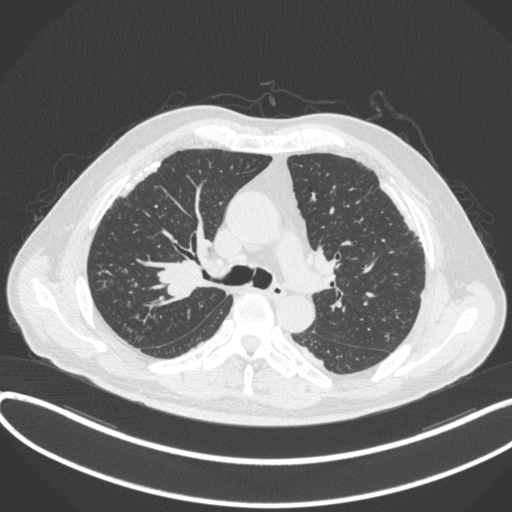
Chest CT, one axial slice. Position 277 of 455 along the scan axis. 120 kVp. Lung window (W 1500 / L -600 HU). 1 mm slice thickness. 512 × 512 image matrix, field of view 400 × 400 mm. Male patient, age 58 years. Case-level facts recorded for this patient, not image findings: clinical TNM (as recorded): T1c N0 M0.
Structures marked on this image (rectangle marked by the reading radiologist):
- lung tumour (recorded histology: squamous cell carcinoma): bounding box <152,254,203,305> (left, top, right, bottom; pixels)